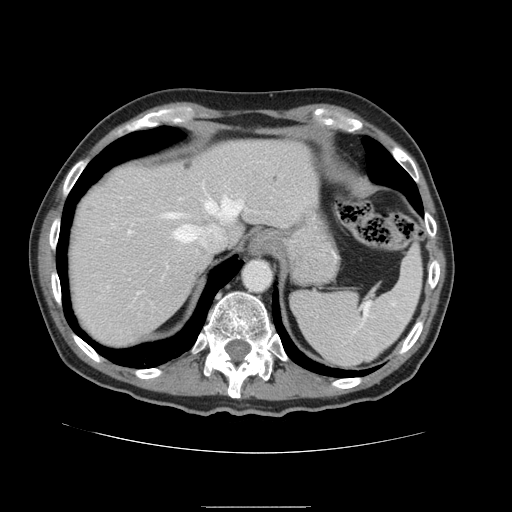
Contrast-enhanced abdominal CT, one axial slice; slice 123 of 168 in the series (ordered by position); 120 kVp; intravenous contrast given; soft-tissue window (W 400 / L 40 HU); 2.5 mm slice thickness; 512 × 512 image matrix, field of view 386 × 386 mm. Male patient, age 74 years. Case-level facts recorded for this patient, not image findings: diagnosis: colorectal cancer liver metastases, imaged before liver resection; multiple liver metastases: no; largest metastasis: 14.5 cm; chemotherapy before resection: no.
Structures marked on this image (expert manual segmentation):
- hepatic veins: bounding box [x1, y1, x2, y2] px = [166, 198, 241, 245]
- liver: [68, 141, 319, 348]
- planned liver remnant (the part of the liver to remain after resection): [68, 140, 319, 348]